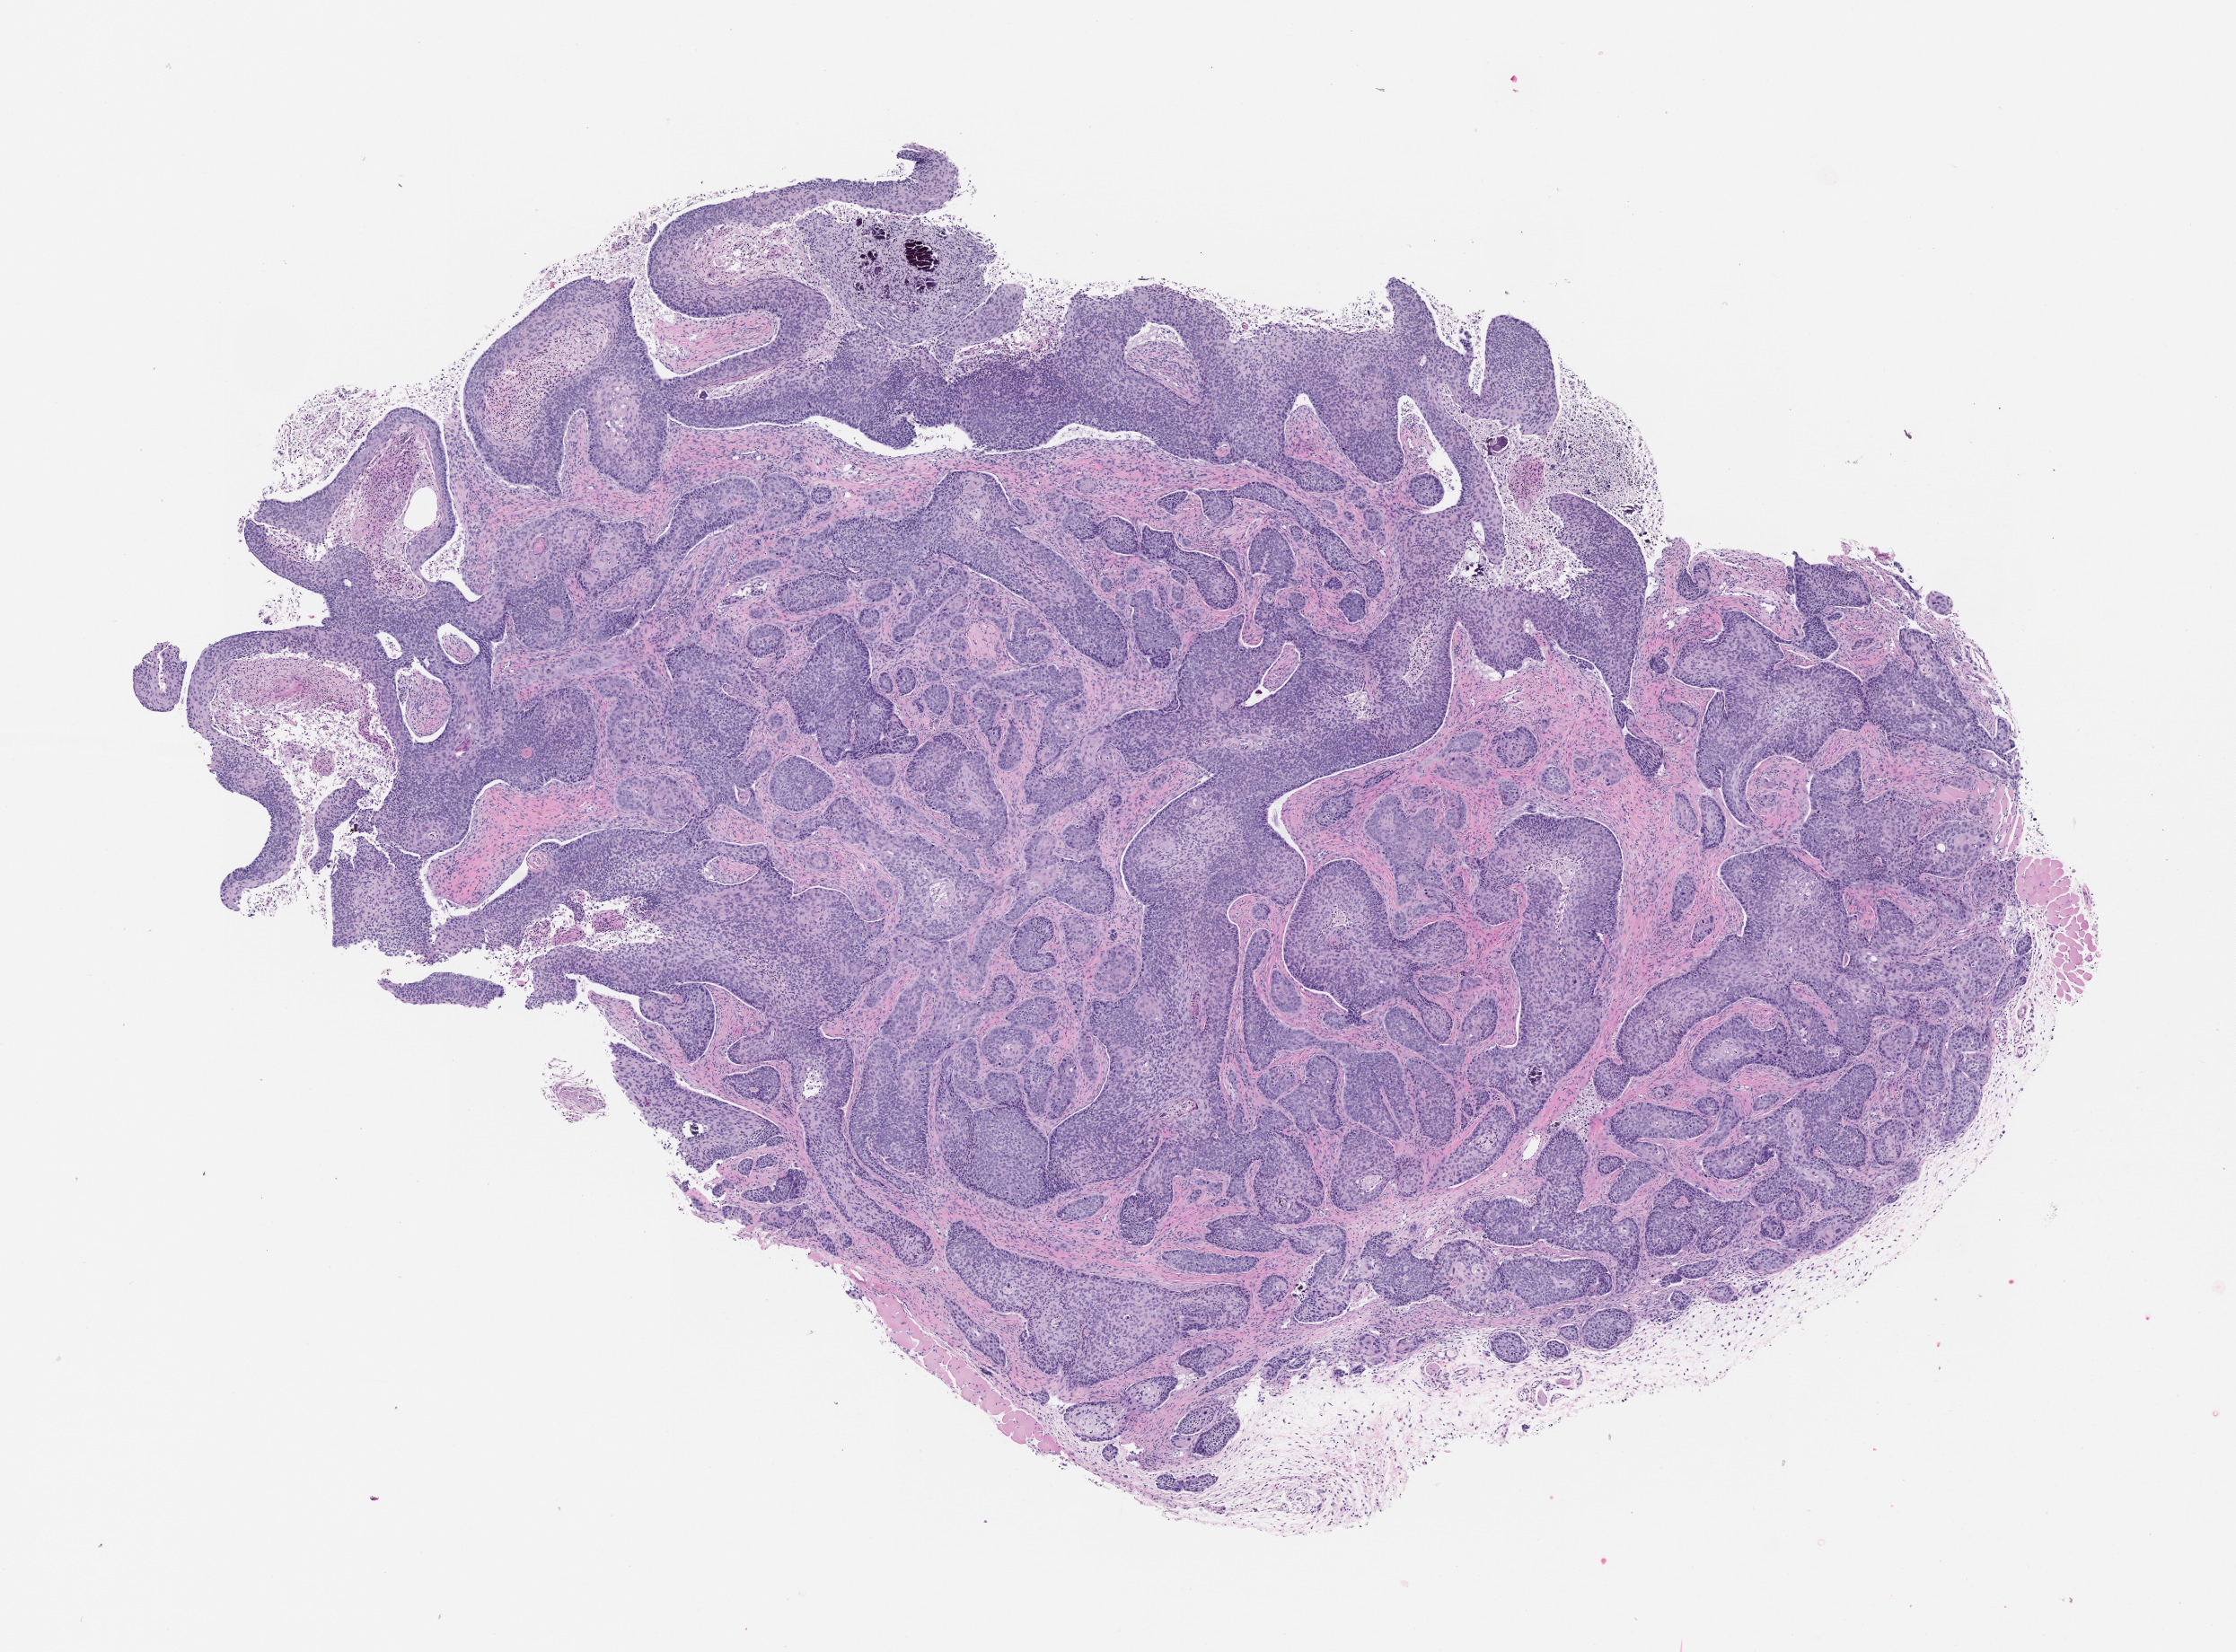
Whole-slide image, haematoxylin and eosin: patient-derived xenograft (human tumor grown in a mouse), passage 0 — shown as a low-resolution overview of the whole scanned area (about 10.0 x 7.4 mm). FFPE section. Tumor site category: head and neck.
Originating patient diagnosis: Head and Neck Squamous Cell Carcinoma.